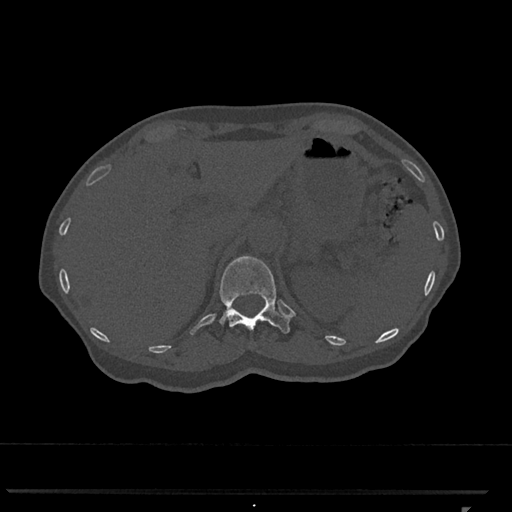
CT including the spine, one axial slice; slice 462 of 793 in the series (ordered by position); 120 kVp; bone window (W 1800 / L 400 HU); 0.5 mm slice thickness; 512 × 512 image matrix, field of view 380 × 380 mm. Patient: female, 62 years. From the clinical record (not read from this slice): primary cancer: renal.
Structures marked on this image (semi-automatic segmentation, software-assisted and operator-edited):
- T12 vertebra: bounding box [x1, y1, x2, y2] px = [213, 256, 290, 334]